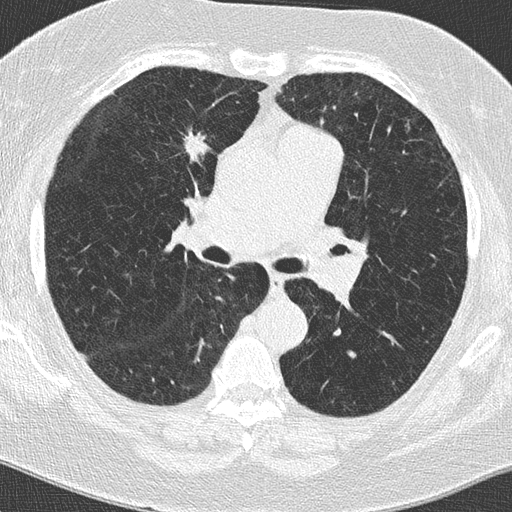
Chest CT (low-dose screening protocol), one axial image. Second annual screen. Lung window (W 1500 / L -600 HU). 2 mm slice thickness. Lung (sharp) reconstruction kernel (B50f). 120 kVp. Slice 59 of 152 in the series. 512 × 512 image matrix. Female, age 62 years at enrolment. Current smoker at enrolment.
- Expert-annotated lung lesion, bounding box (x1, y1, x2, y2) in pixels: (160, 115, 227, 175).
- The screening reader recorded 2 non-calcified nodules or masses ≥4 mm on this exam (left lower lobe, right middle lobe); which of them this box marks is not recorded.